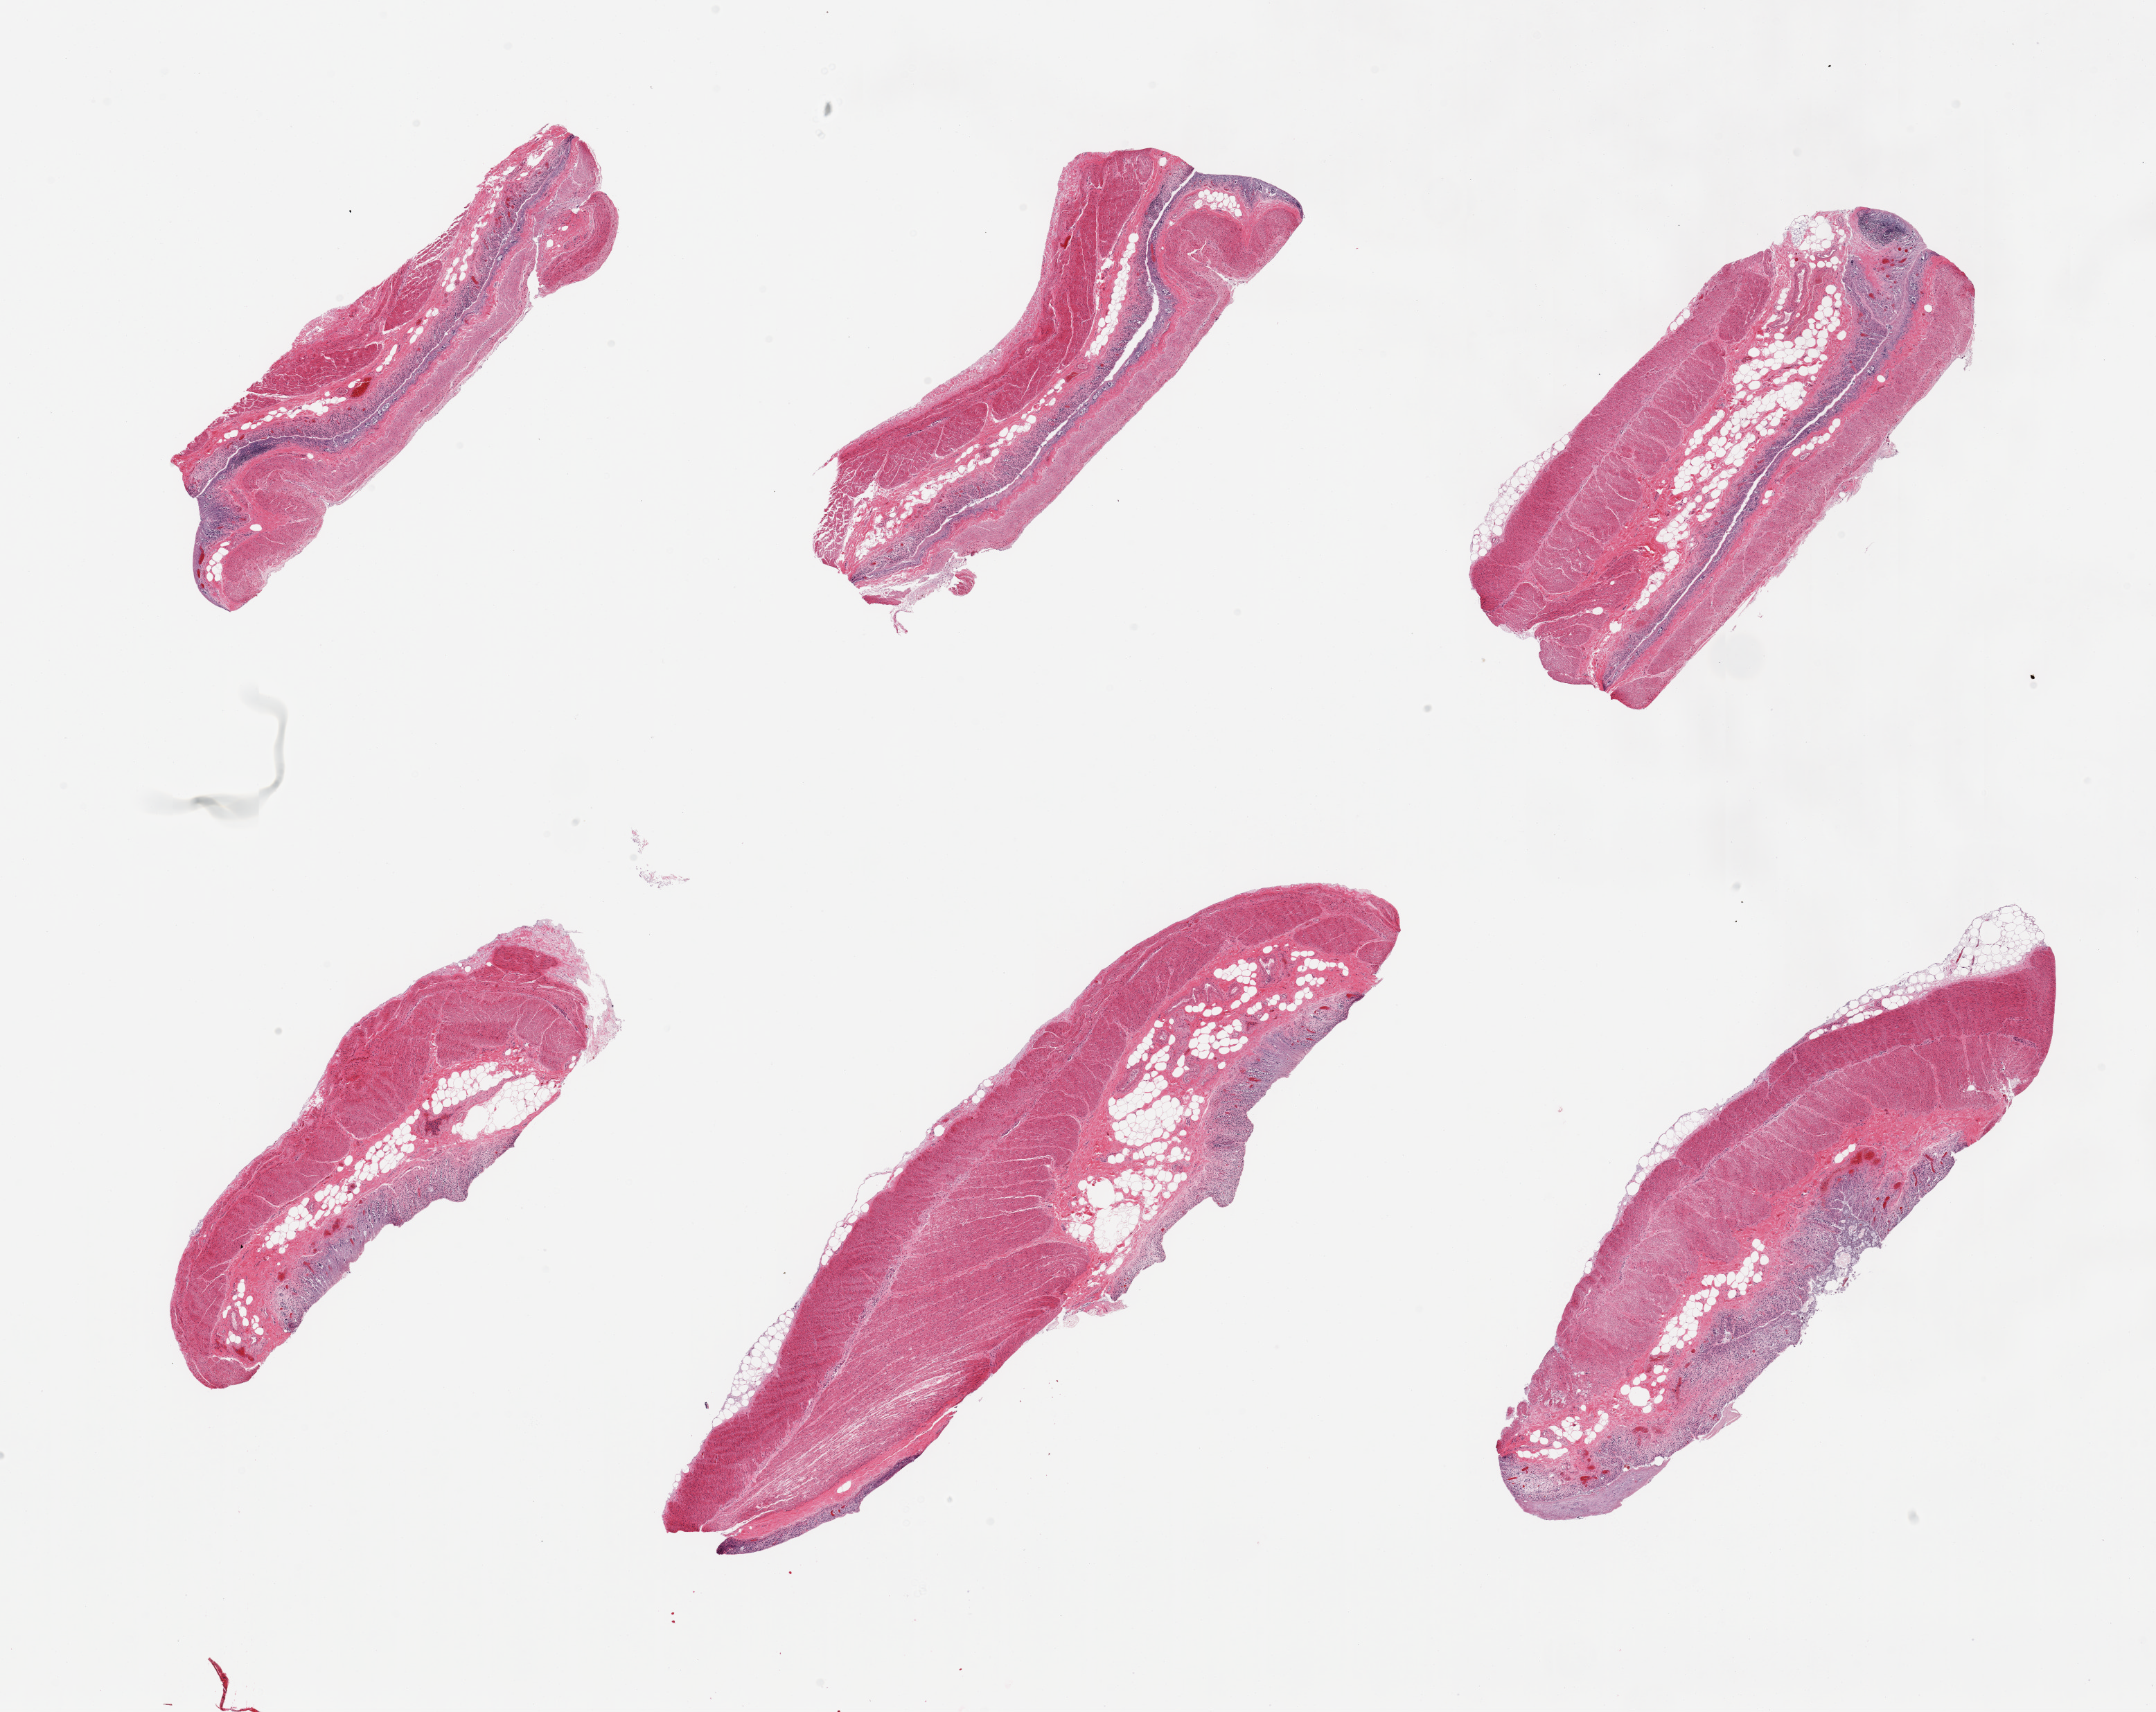
Whole-slide image, haematoxylin and eosin stain — shown as a low-resolution overview of the whole scanned area (about 24.6 x 19.5 mm); PAXgene-fixed, paraffin-embedded tissue; sampled site (target tissue): transverse colon; donor tissue sample. Donor: male.
Review note (as recorded): 6 pieces; autolyzed mucosa grade 3; muscularis intact.